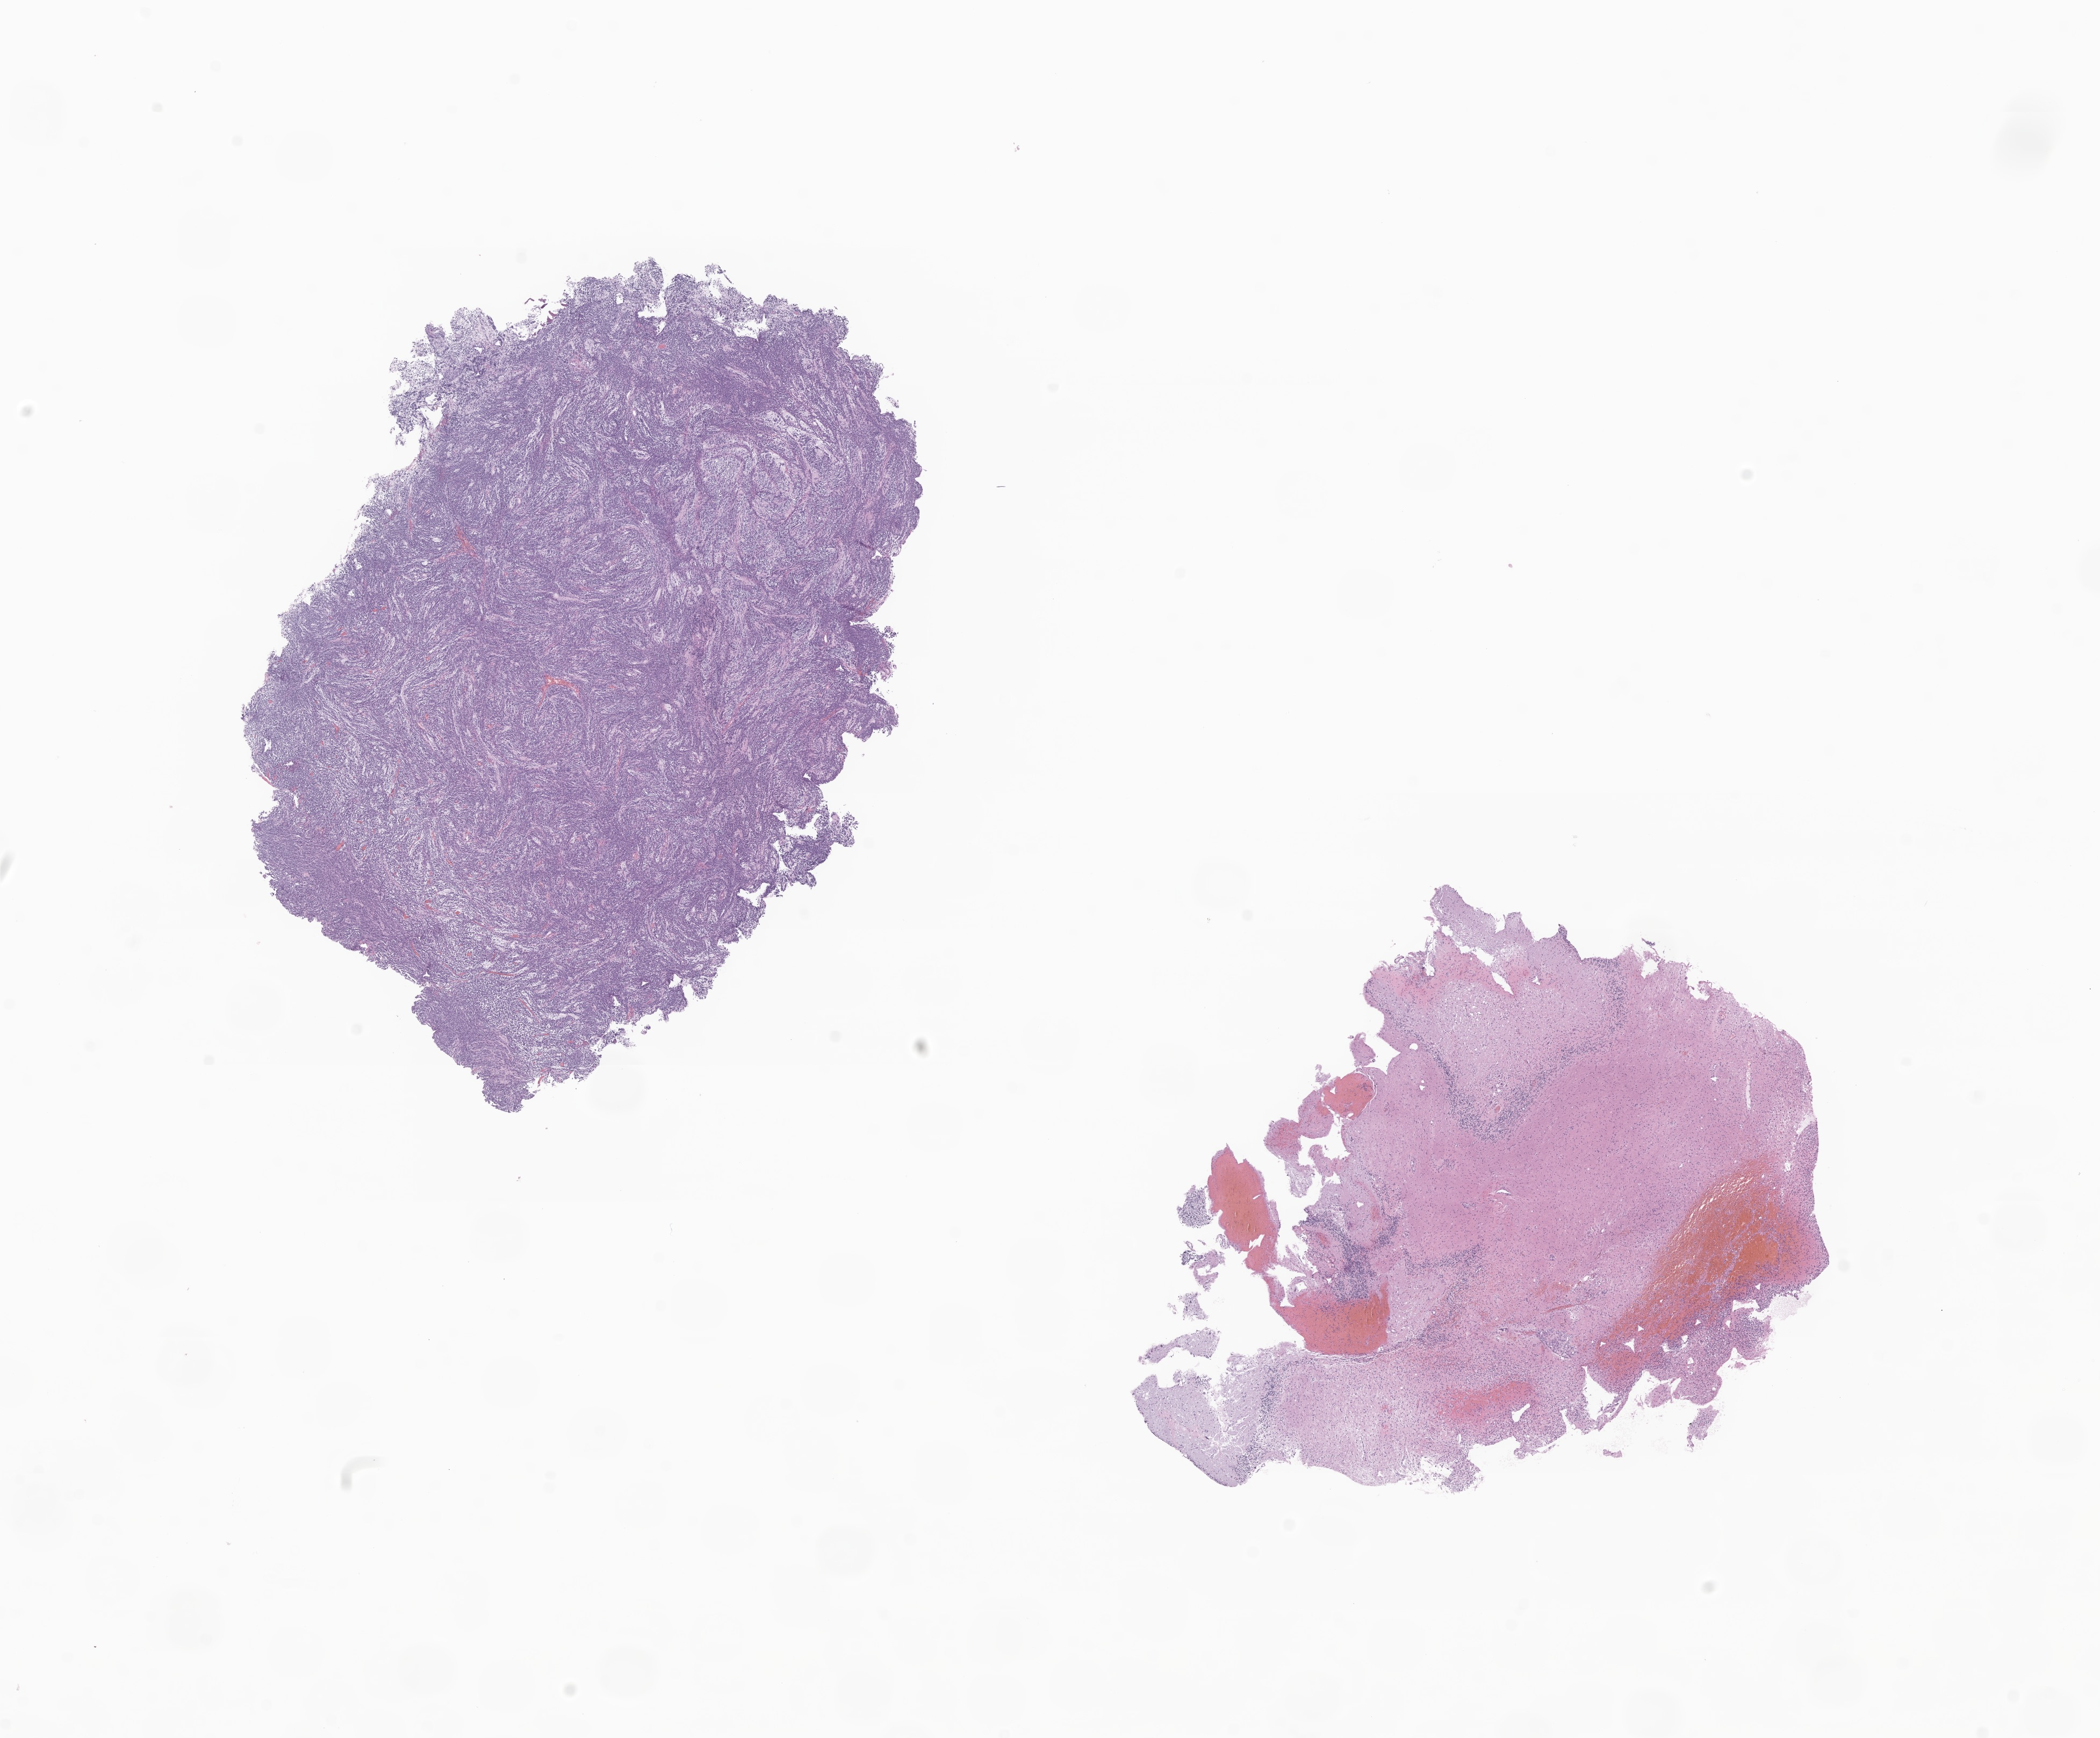
Haematoxylin and eosin whole-slide image of tumor tissue from the cerebellum, a low-resolution overview of the entire scanned area, about 16.5 x 13.6 mm; formalin-fixed paraffin-embedded section. Male patient, age 697 days (about 1.9 years).
Recorded diagnosis: Desmoplastic nodular medulloblastoma.